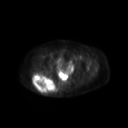
FDG PET of an extremity soft-tissue mass (from a PET/CT study), one axial slice; slice 56 of 267 in the series (ordered by position); 3.27 mm slice thickness; 128 × 128 image matrix, field of view 600 × 600 mm. Female patient, age 60 years. Case-level facts recorded for this patient, not image findings: histological type: spindle cell suggestive of myxofibrosarcoma; grade: intermediate; site of the primary tumour: right buttock.
Structures marked on this image (expert contour drawn on MRI and transferred to this co-registered scan by the dataset authors):
- gross tumour volume (mass): bounding box (x1, y1, x2, y2) in pixels: (33, 73, 57, 94)